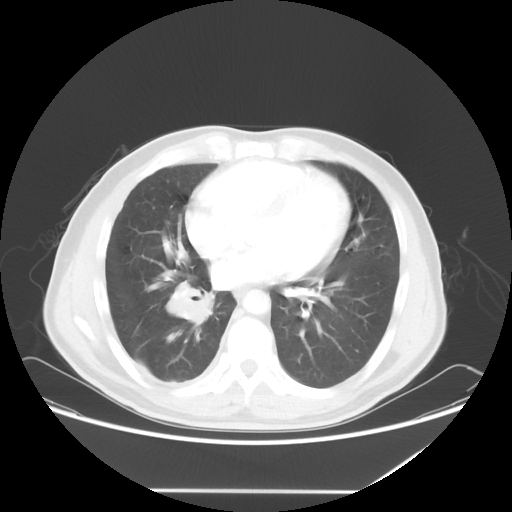
Chest CT, one axial slice; slice 25 of 60 in the series (ordered by position); lung window (W 1500 / L -600 HU); 512 × 512 image matrix, field of view 419 × 419 mm. Male patient, age 48 years. From the clinical record (not read from this slice): clinical TNM (as recorded): T3 N3 M1a.
Structures marked on this image (rectangle marked by the reading radiologist):
- lung tumour (recorded histology: squamous cell carcinoma): bounding box <162,277,216,334> (left, top, right, bottom; pixels)